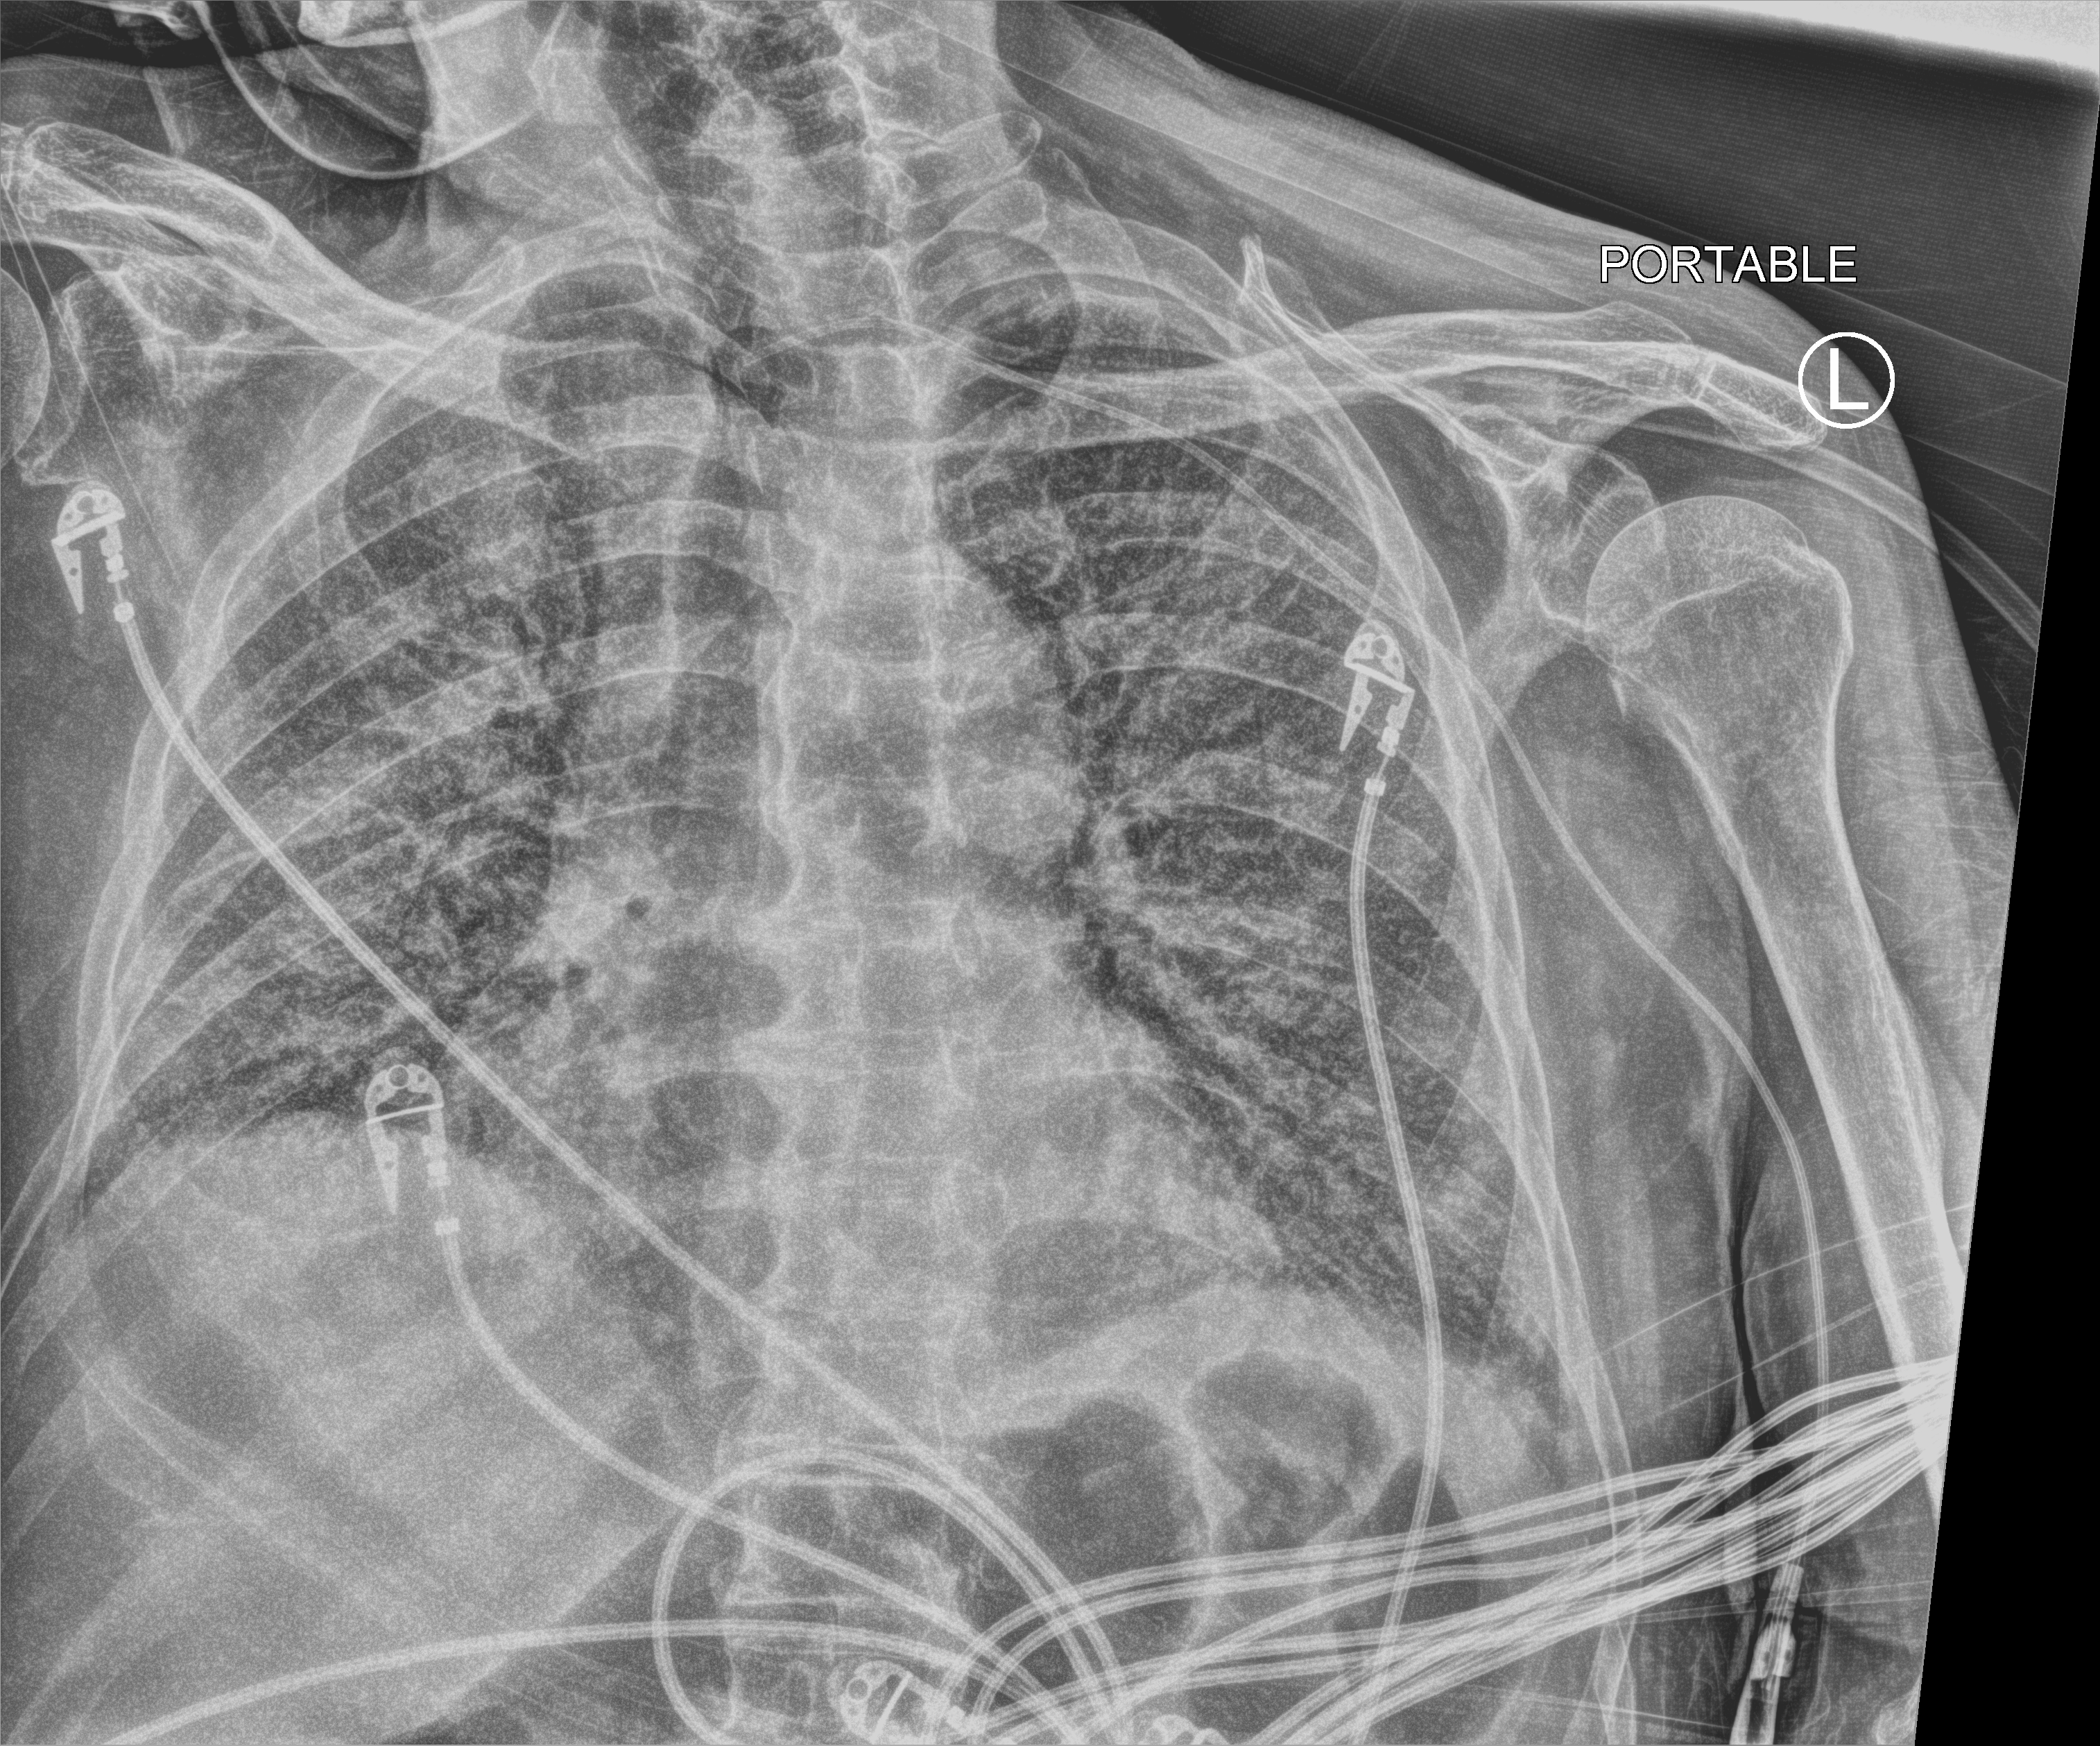
Portable chest radiograph, anteroposterior (AP) projection. Patient hospitalised with COVID-19; male, aged 75–90 years.
Admission-level facts for this patient (not findings on this image; timing relative to this image not recorded): admitted to intensive care during this hospital stay: yes.